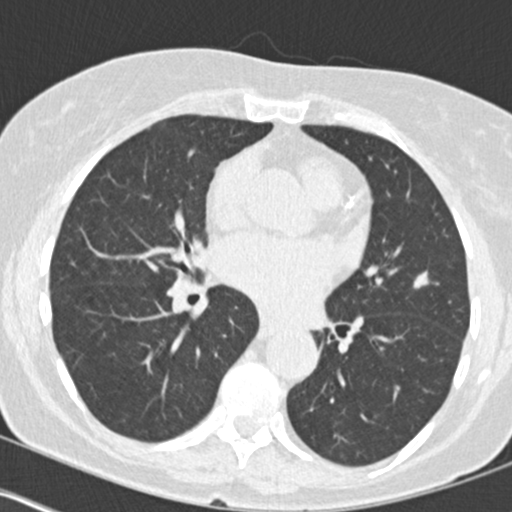
Low-dose screening chest CT, one axial slice; position 83 of 160 along the scan axis; 120 kVp; lung window (W 1500 / L -600 HU); 512 × 512 image matrix.
Structures marked on this image (expert manual segmentation):
- lesion 1 (tumor, upper lobe of left lung): bounding box <414,272,428,288> (left, top, right, bottom; pixels)